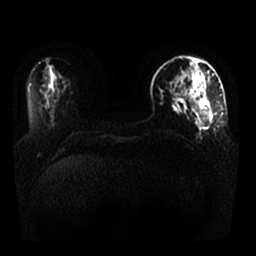
Breast MRI, one axial slice. Diffusion-weighted series; image 2 of 4 stored at this slice position (different b-values; order by instance number). 1.5 T. 4 mm slice thickness. 256 × 256 image matrix, field of view 330 × 330 mm. Female patient.
Outlined on this slice (outlined manually by an expert reader):
- tumour on diffusion-weighted imaging: bounding box <200,99,209,109> (left, top, right, bottom; pixels)